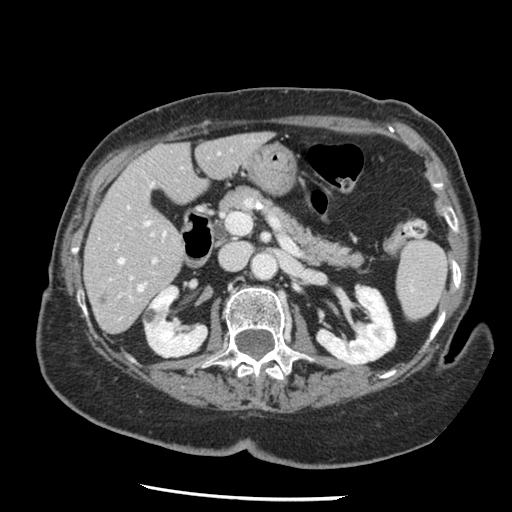
Contrast-enhanced abdominal CT, one axial slice. Position 65 of 148 along the scan axis. Soft-tissue window (W 400 / L 40 HU). 2.5 mm slice thickness. 512 × 512 image matrix. Female patient, age 85 years. Case-level facts recorded for this patient, not image findings: diagnosis: colorectal cancer liver metastases, imaged before liver resection; multiple liver metastases: no; largest metastasis: 0.9 cm.
Outlined on this slice (expert manual segmentation):
- hepatic veins: box from (x=118, y=258) to (x=145, y=291) px
- liver: (x=85, y=134)–(x=268, y=333)
- planned liver remnant (the part of the liver to remain after resection): (x=85, y=134)–(x=268, y=329)
- portal vein (with intrahepatic branches): (x=127, y=206)–(x=158, y=280)
- liver metastasis: (x=99, y=294)–(x=110, y=303)